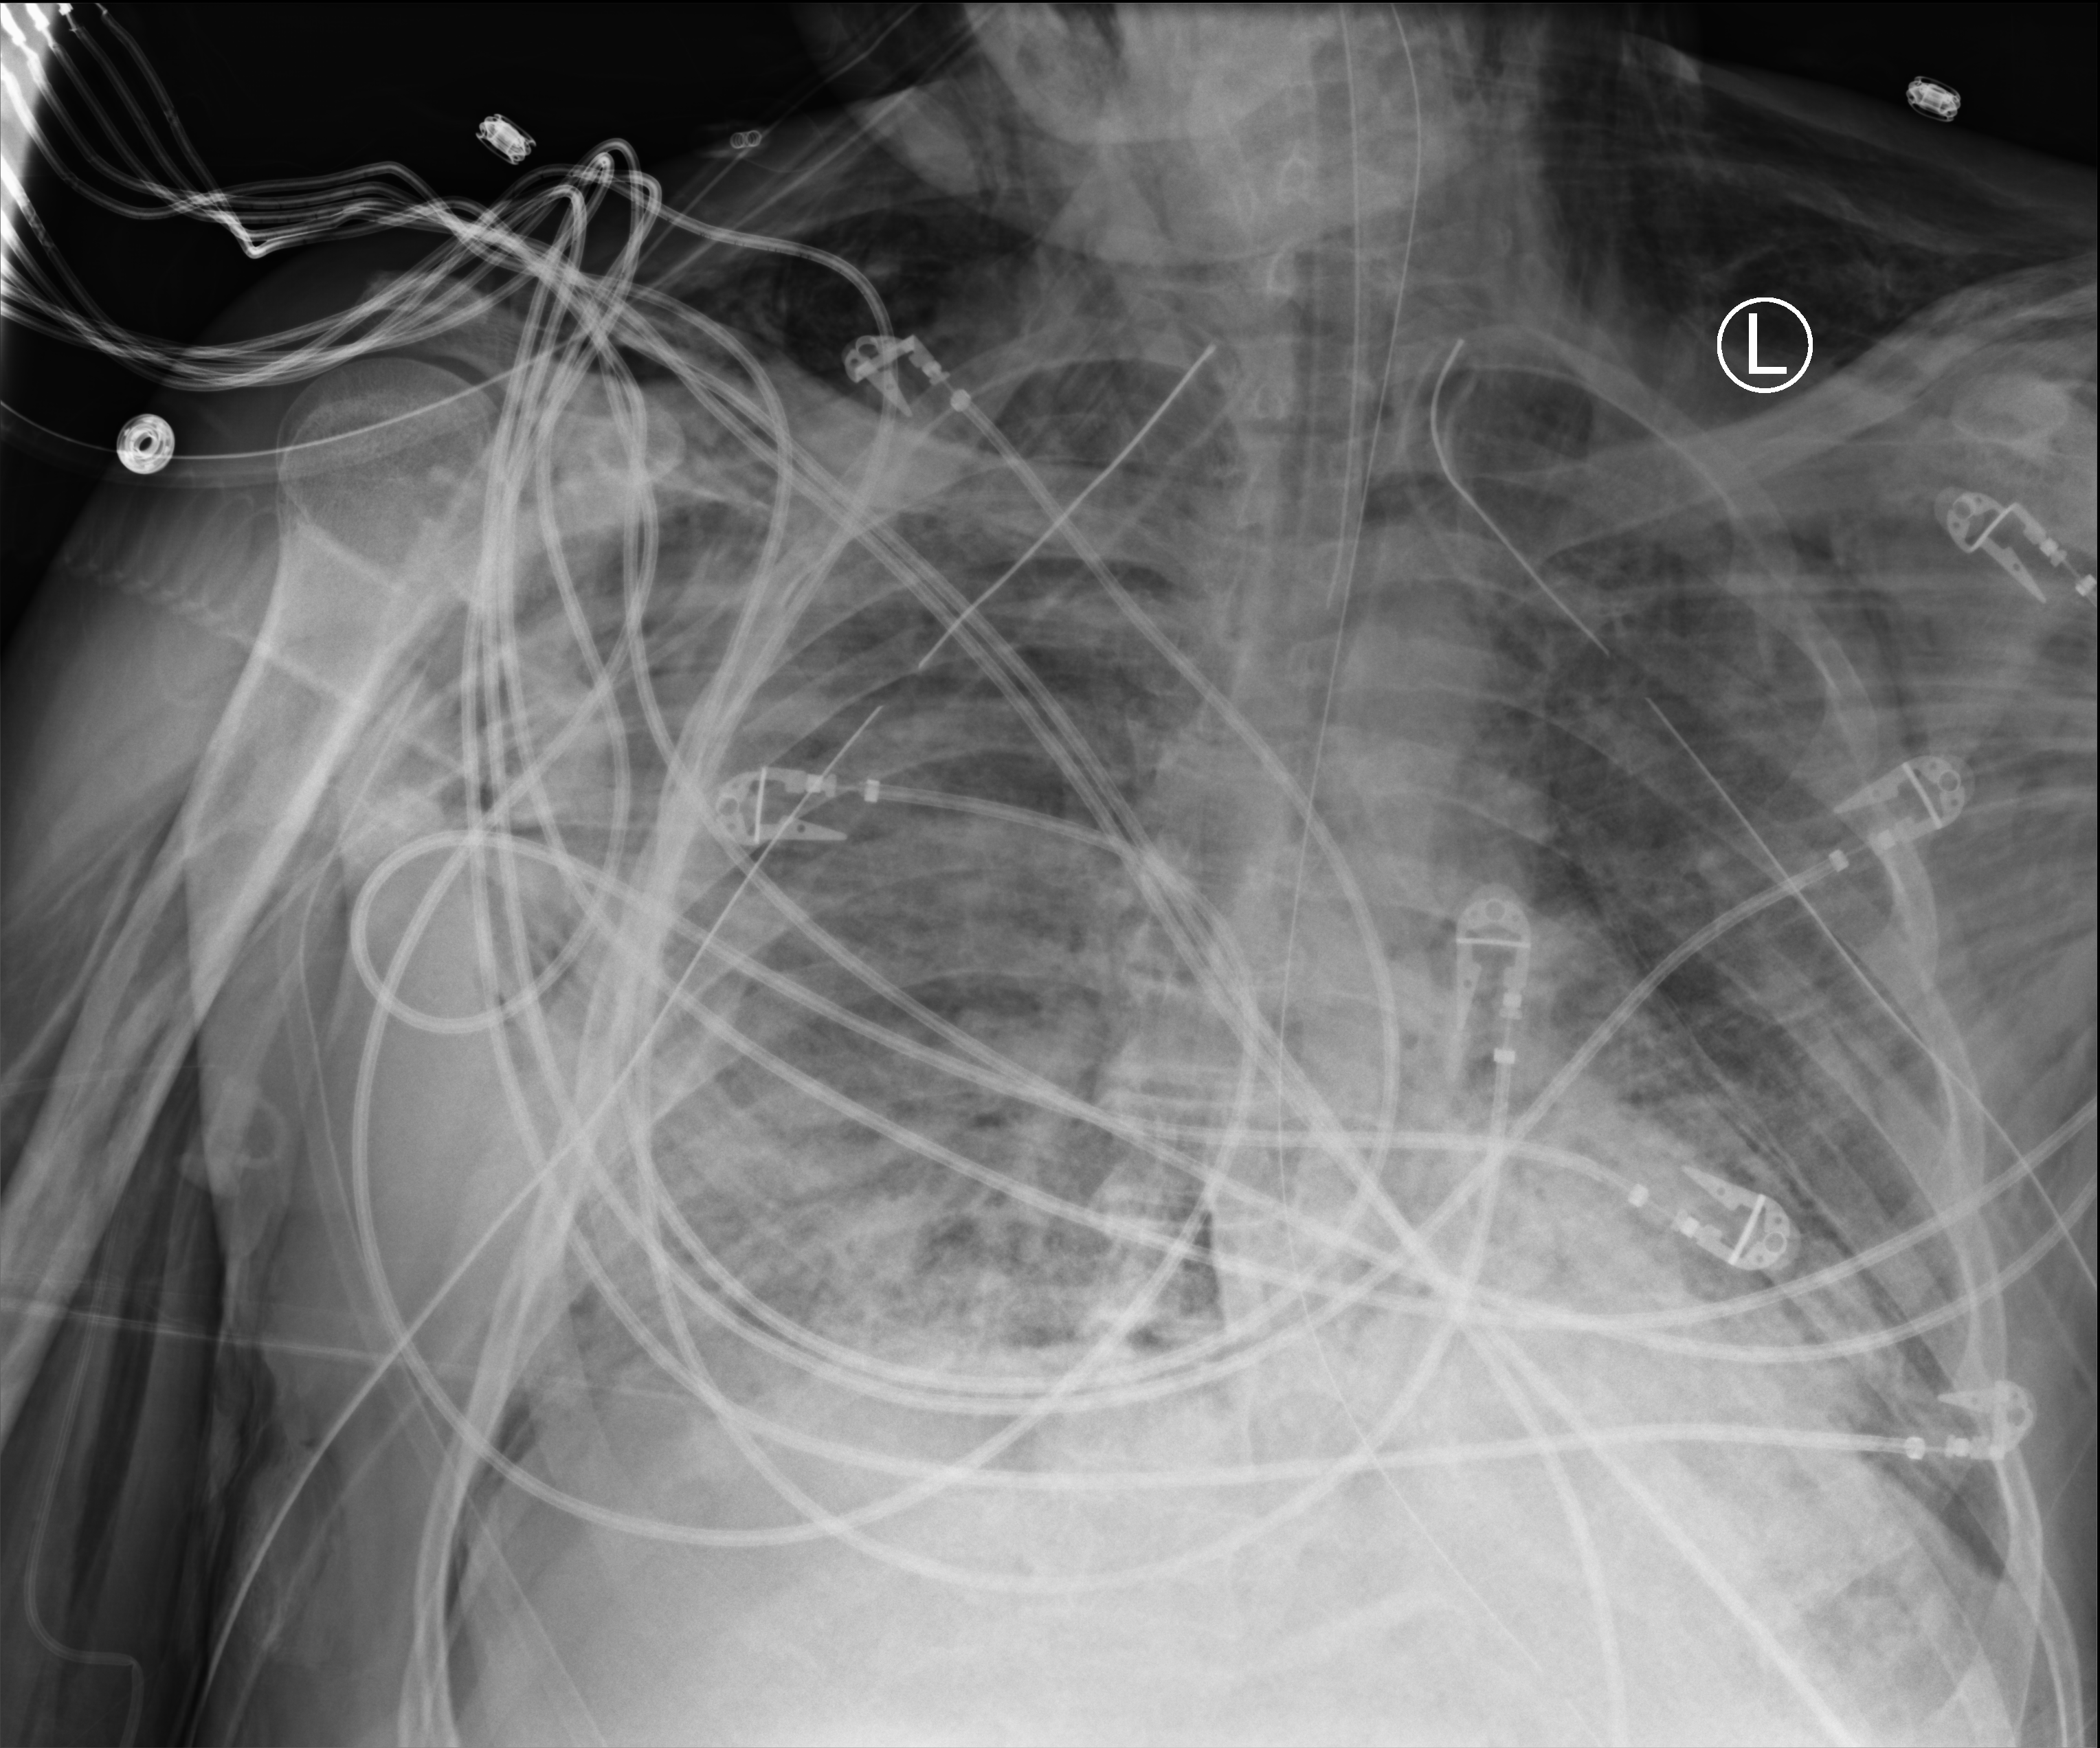
Chest X-ray (portable). Patient hospitalised with COVID-19; male, aged 18–59 years.
From the hospital-stay record, not from the radiograph (when in the stay this image was taken is not recorded):
- mechanically ventilated during this hospital stay: yes
- hypertension (admission record): yes